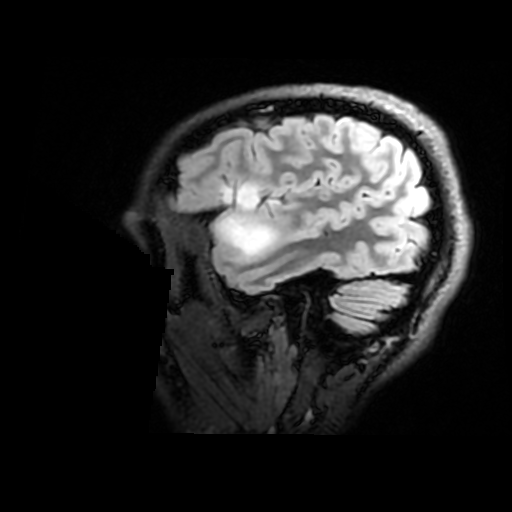
Brain MRI from a brain-tumour surgery series, one sagittal slice; position 138 of 176 along the scan axis; T2 FLAIR; 1 mm slice thickness; 512 × 512 image matrix, field of view 240 × 240 mm. From the clinical record (not read from this slice): histopathology: Astrocytoma; WHO grade: 2; IDH mutation: yes; tumour location: Right Insular.
Annotated regions visible in this slice (manually delineated by an expert):
- tumour: box from (x=223, y=185) to (x=280, y=259) px